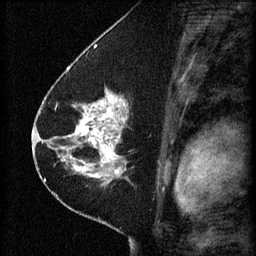
Breast MRI (dynamic contrast-enhanced), one sagittal slice. 3 images stored at this slice position (order not interpretable as contrast timing). 1.5 T. TE 4.2 ms, TR 8.2 ms. 256 × 256 image matrix, field of view 180 × 180 mm. Patient: female, 41 years.
Structures marked on this image (semi-automatic segmentation, software-assisted and operator-edited):
- analysis volume of interest (the breast-tissue region the enhancement analysis was run in; not a lesion): bounding box [x1, y1, x2, y2] px = [67, 92, 165, 173]
- tumour enhancement mask (voxels above the 70 % enhancement threshold inside the analysis volume of interest): [72, 92, 127, 173]